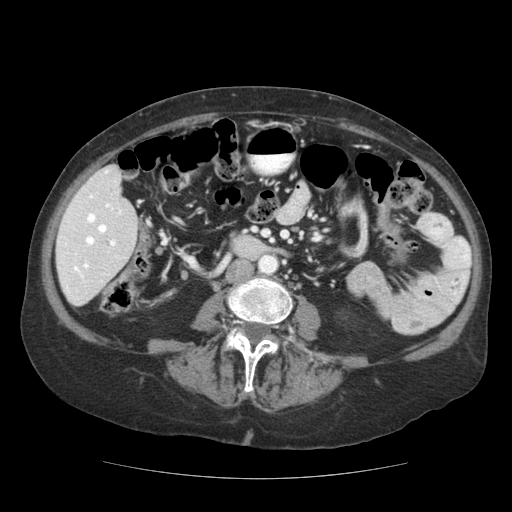
Contrast-enhanced abdominal CT (liver protocol), one axial slice. Slice 40 of 111 in the series (ordered by position). 140 kVp. Soft-tissue window (W 400 / L 40 HU). 2.5 mm slice thickness. 512 × 512 image matrix, field of view 360 × 360 mm. Case-level facts recorded for this patient, not image findings: diagnosis: hepatocellular carcinoma (patient treated with transarterial chemoembolisation; whether this scan precedes or follows treatment is not stated here); TNM stage (as recorded): Stage-I; Child-Pugh class: A; tumour differentiation: moderately-poorly differentiated; tumour nodularity: uninodular.
Structures marked on this image (semi-automatically segmented with operator editing):
- liver parenchyma outside the tumour (the mass and vessels are separate outlines, so this box may not span the whole liver): bounding box (x1, y1, x2, y2) in pixels: (56, 164, 138, 306)
- liver vessels: (65, 171, 121, 292)